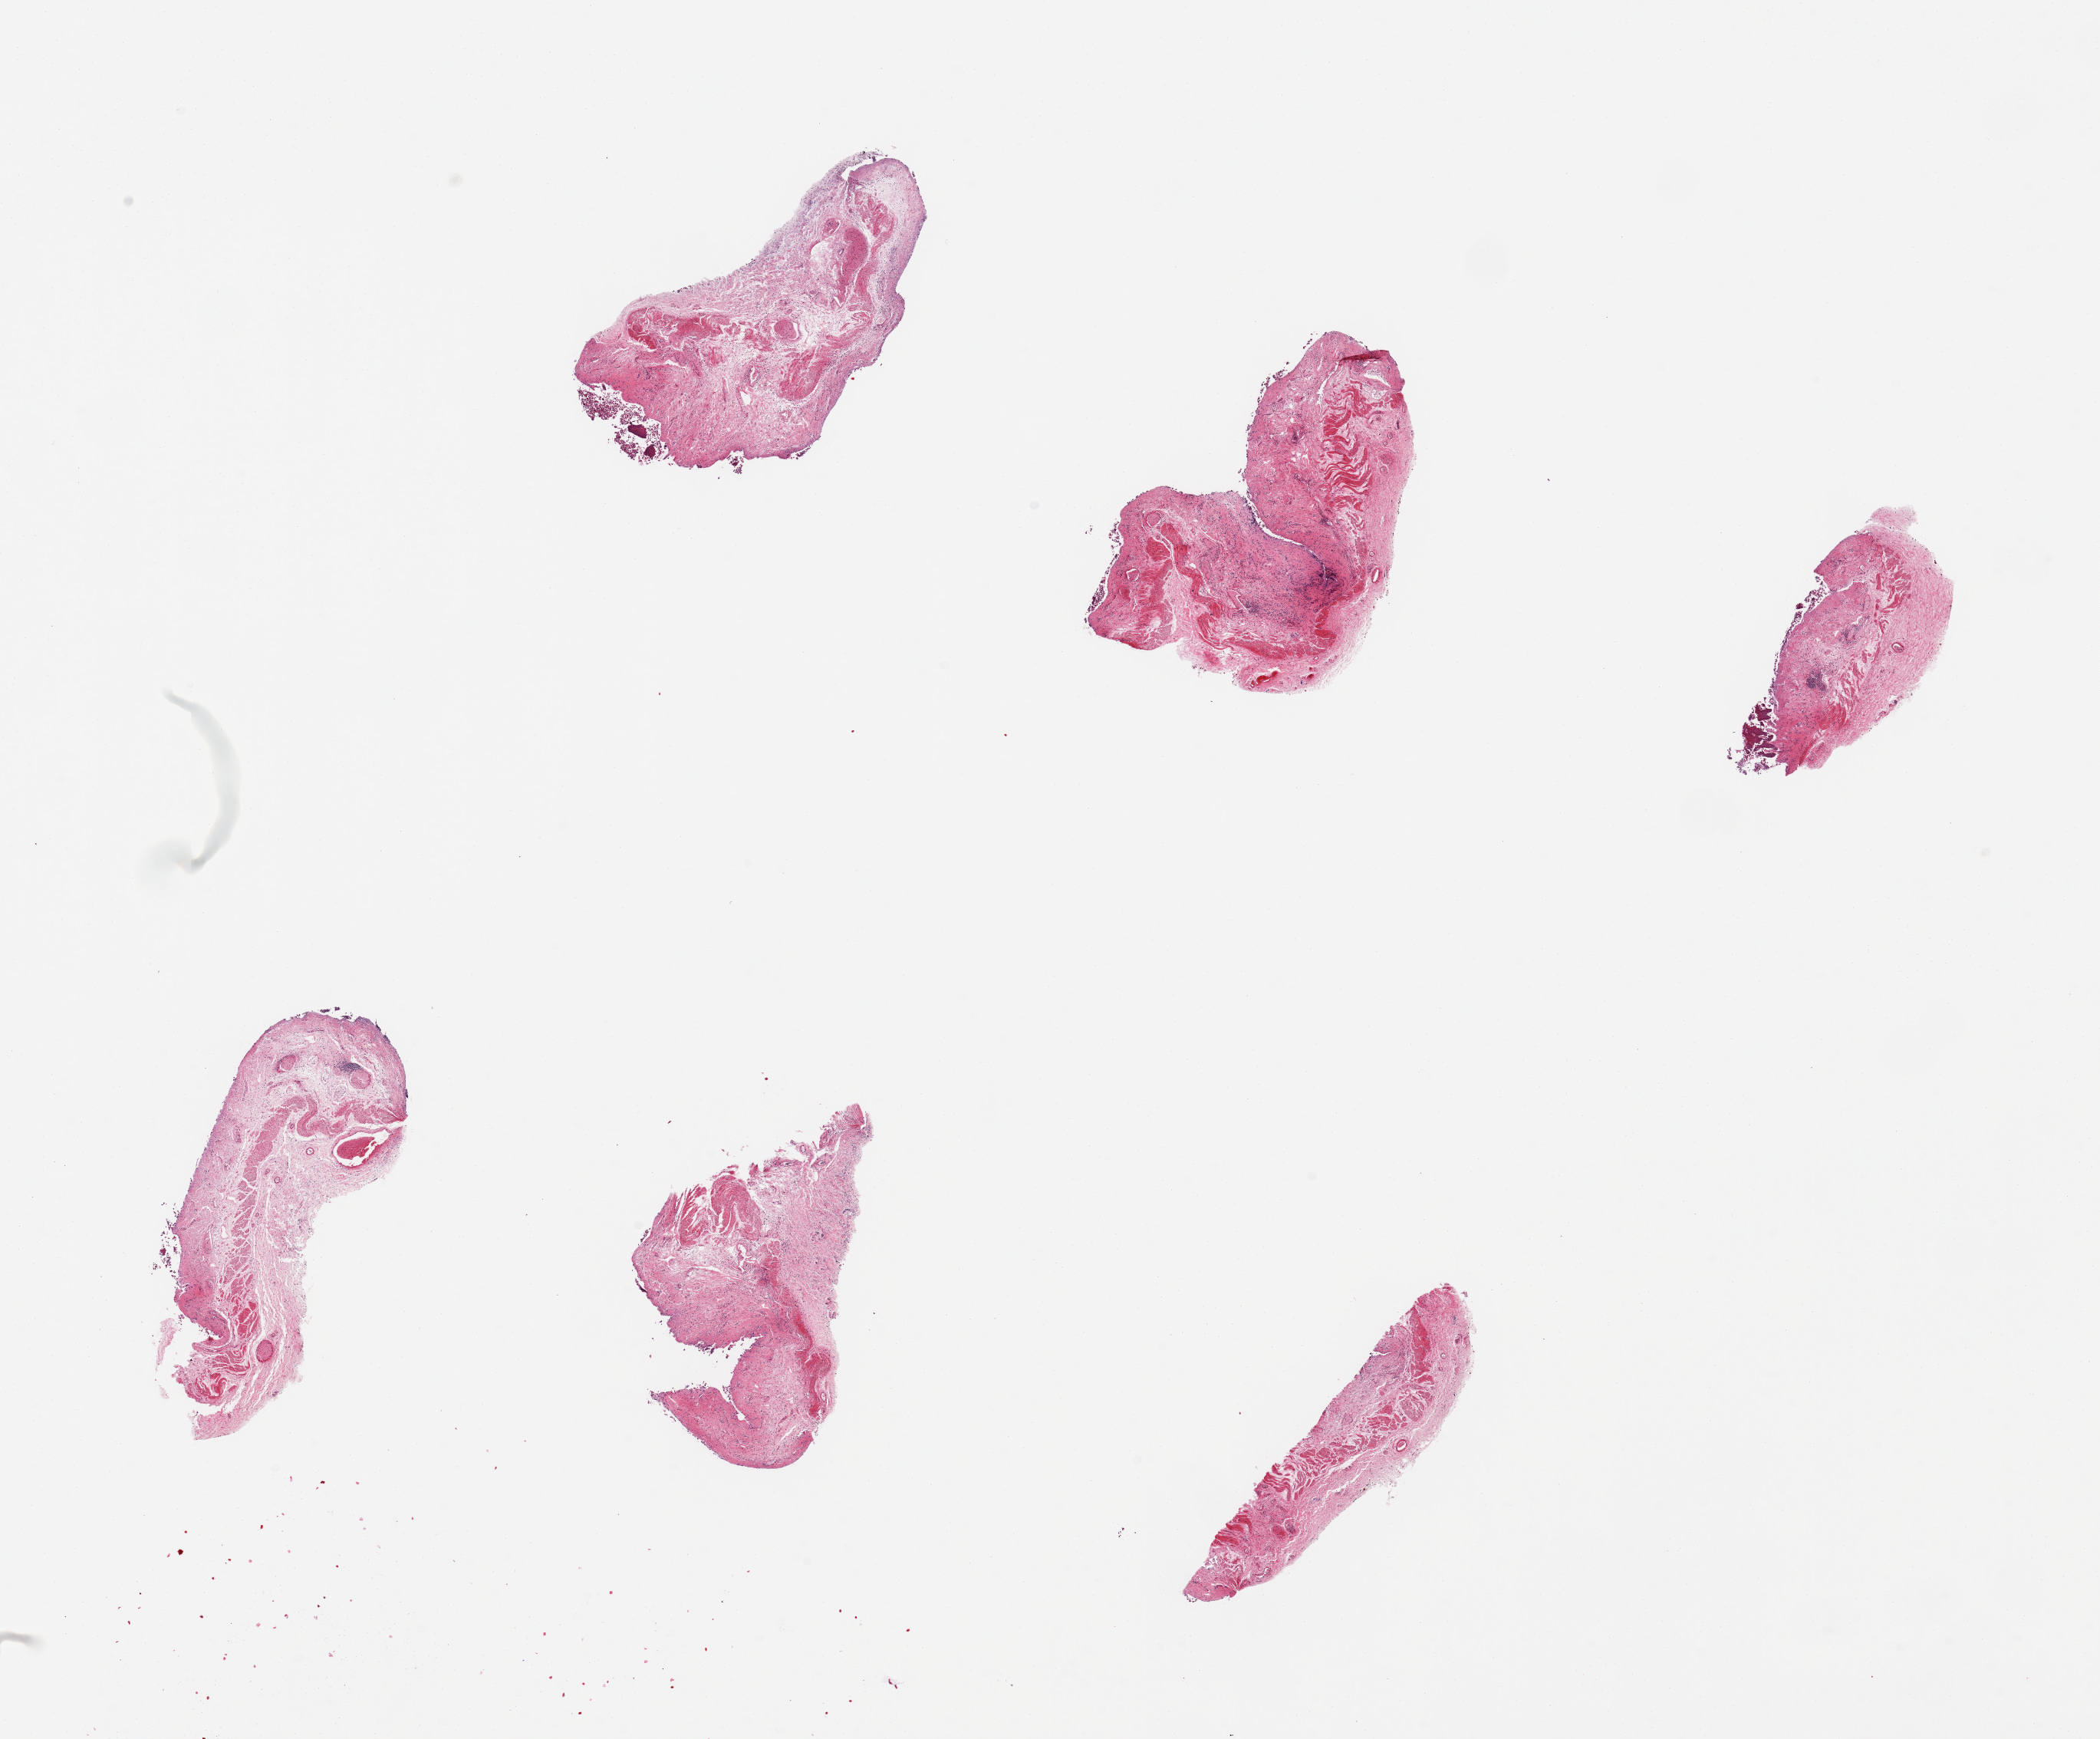
Whole-slide image, hematoxylin and eosin (H&E) stain — whole scanned area (about 21.7 x 17.9 mm, from a 20x scan) shown as a low-resolution overview; PAXgene-fixed paraffin-embedded (PFPE) section; section of esophageal mucous membrane (target tissue); donor tissue sample. Donor: male.
Reviewer comment on this tissue sample: 6 pieces, minimal evident muscle; edematous fat/fibrous tissue, badly autolyzed, uncertain provenance.